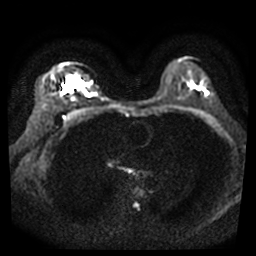
Breast MRI, one axial slice. Position 25 of 40 along the scan axis. Diffusion-weighted series; image 2 of 4 stored at this slice position (different b-values; order by instance number). 3 T. 256 × 256 image matrix. Female patient.
Annotated regions visible in this slice (expert manual segmentation):
- tumour on diffusion-weighted imaging: bounding box (x1, y1, x2, y2) in pixels: (65, 80, 74, 91)